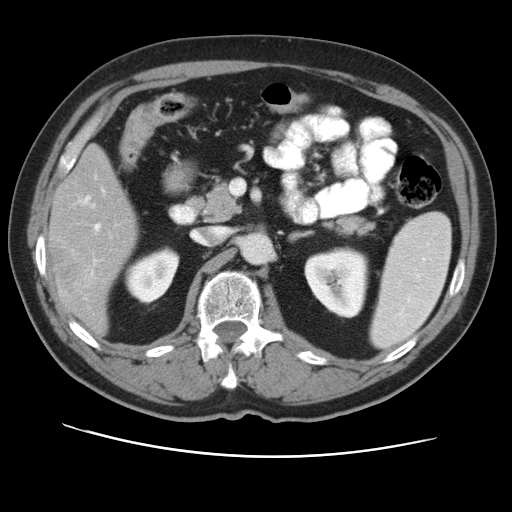
Contrast-enhanced abdominal CT, one axial slice. Position 22 of 49 along the scan axis. Reconstruction kernel STANDARD. Intravenous contrast given. Soft-tissue window (W 400 / L 40 HU). 5 mm slice thickness. 512 × 512 image matrix, field of view 374 × 374 mm. Male patient, age 59 years. From the clinical record (not read from this slice): diagnosis: colorectal cancer liver metastases, imaged before liver resection; multiple liver metastases: yes; largest metastasis: 6.3 cm; chemotherapy before resection: yes.
Structures marked on this image (outlined manually by an expert reader):
- hepatic veins: bounding box <83,197,90,203> (left, top, right, bottom; pixels)
- liver: <51,149,137,332>
- planned liver remnant (the part of the liver to remain after resection): <54,149,137,251>
- portal vein (with intrahepatic branches): <92,223,100,273>
- liver metastasis: <54,245,89,293>